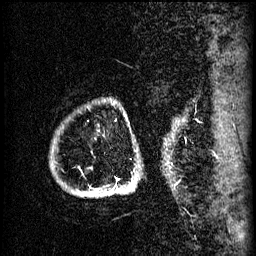
Breast MRI (dynamic contrast-enhanced), one sagittal slice; slice 58 of 60 in the series (ordered by position); 3 images stored at this slice position (order not interpretable as contrast timing); 1.5 T; TE 4.2 ms, TR 11 ms; 2 mm slice thickness; 256 × 256 image matrix, field of view 200 × 200 mm. Patient: female, 51 years.
Outlined on this slice (semi-automatically segmented with operator editing):
- analysis volume of interest (the breast-tissue region the enhancement analysis was run in; not a lesion): box from (x=79, y=178) to (x=136, y=197) px
- tumour enhancement mask (voxels above the 70 % enhancement threshold inside the analysis volume of interest): (x=118, y=178)–(x=121, y=181)